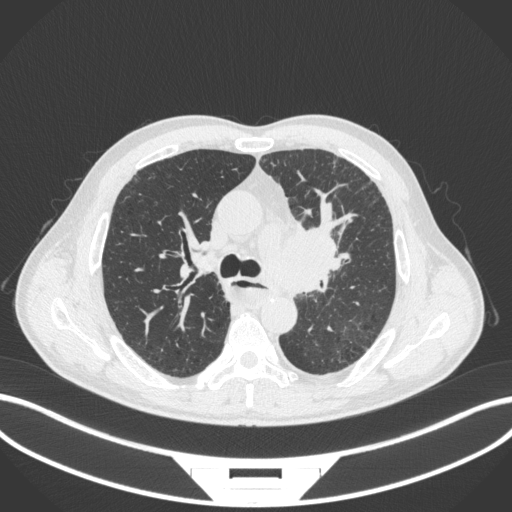
Chest CT, one axial slice; slice 250 of 411 in the series (ordered by position); reconstruction kernel B31f; 120 kVp; lung window (W 1500 / L -600 HU); 1 mm slice thickness; 512 × 512 image matrix, field of view 400 × 400 mm. Male patient, age 57 years. From the clinical record (not read from this slice): clinical TNM (as recorded): T2a N1 M0.
Structures marked on this image (bounding box drawn by a radiologist):
- lung tumour (recorded histology: squamous cell carcinoma): bounding box <259,218,347,289> (left, top, right, bottom; pixels)